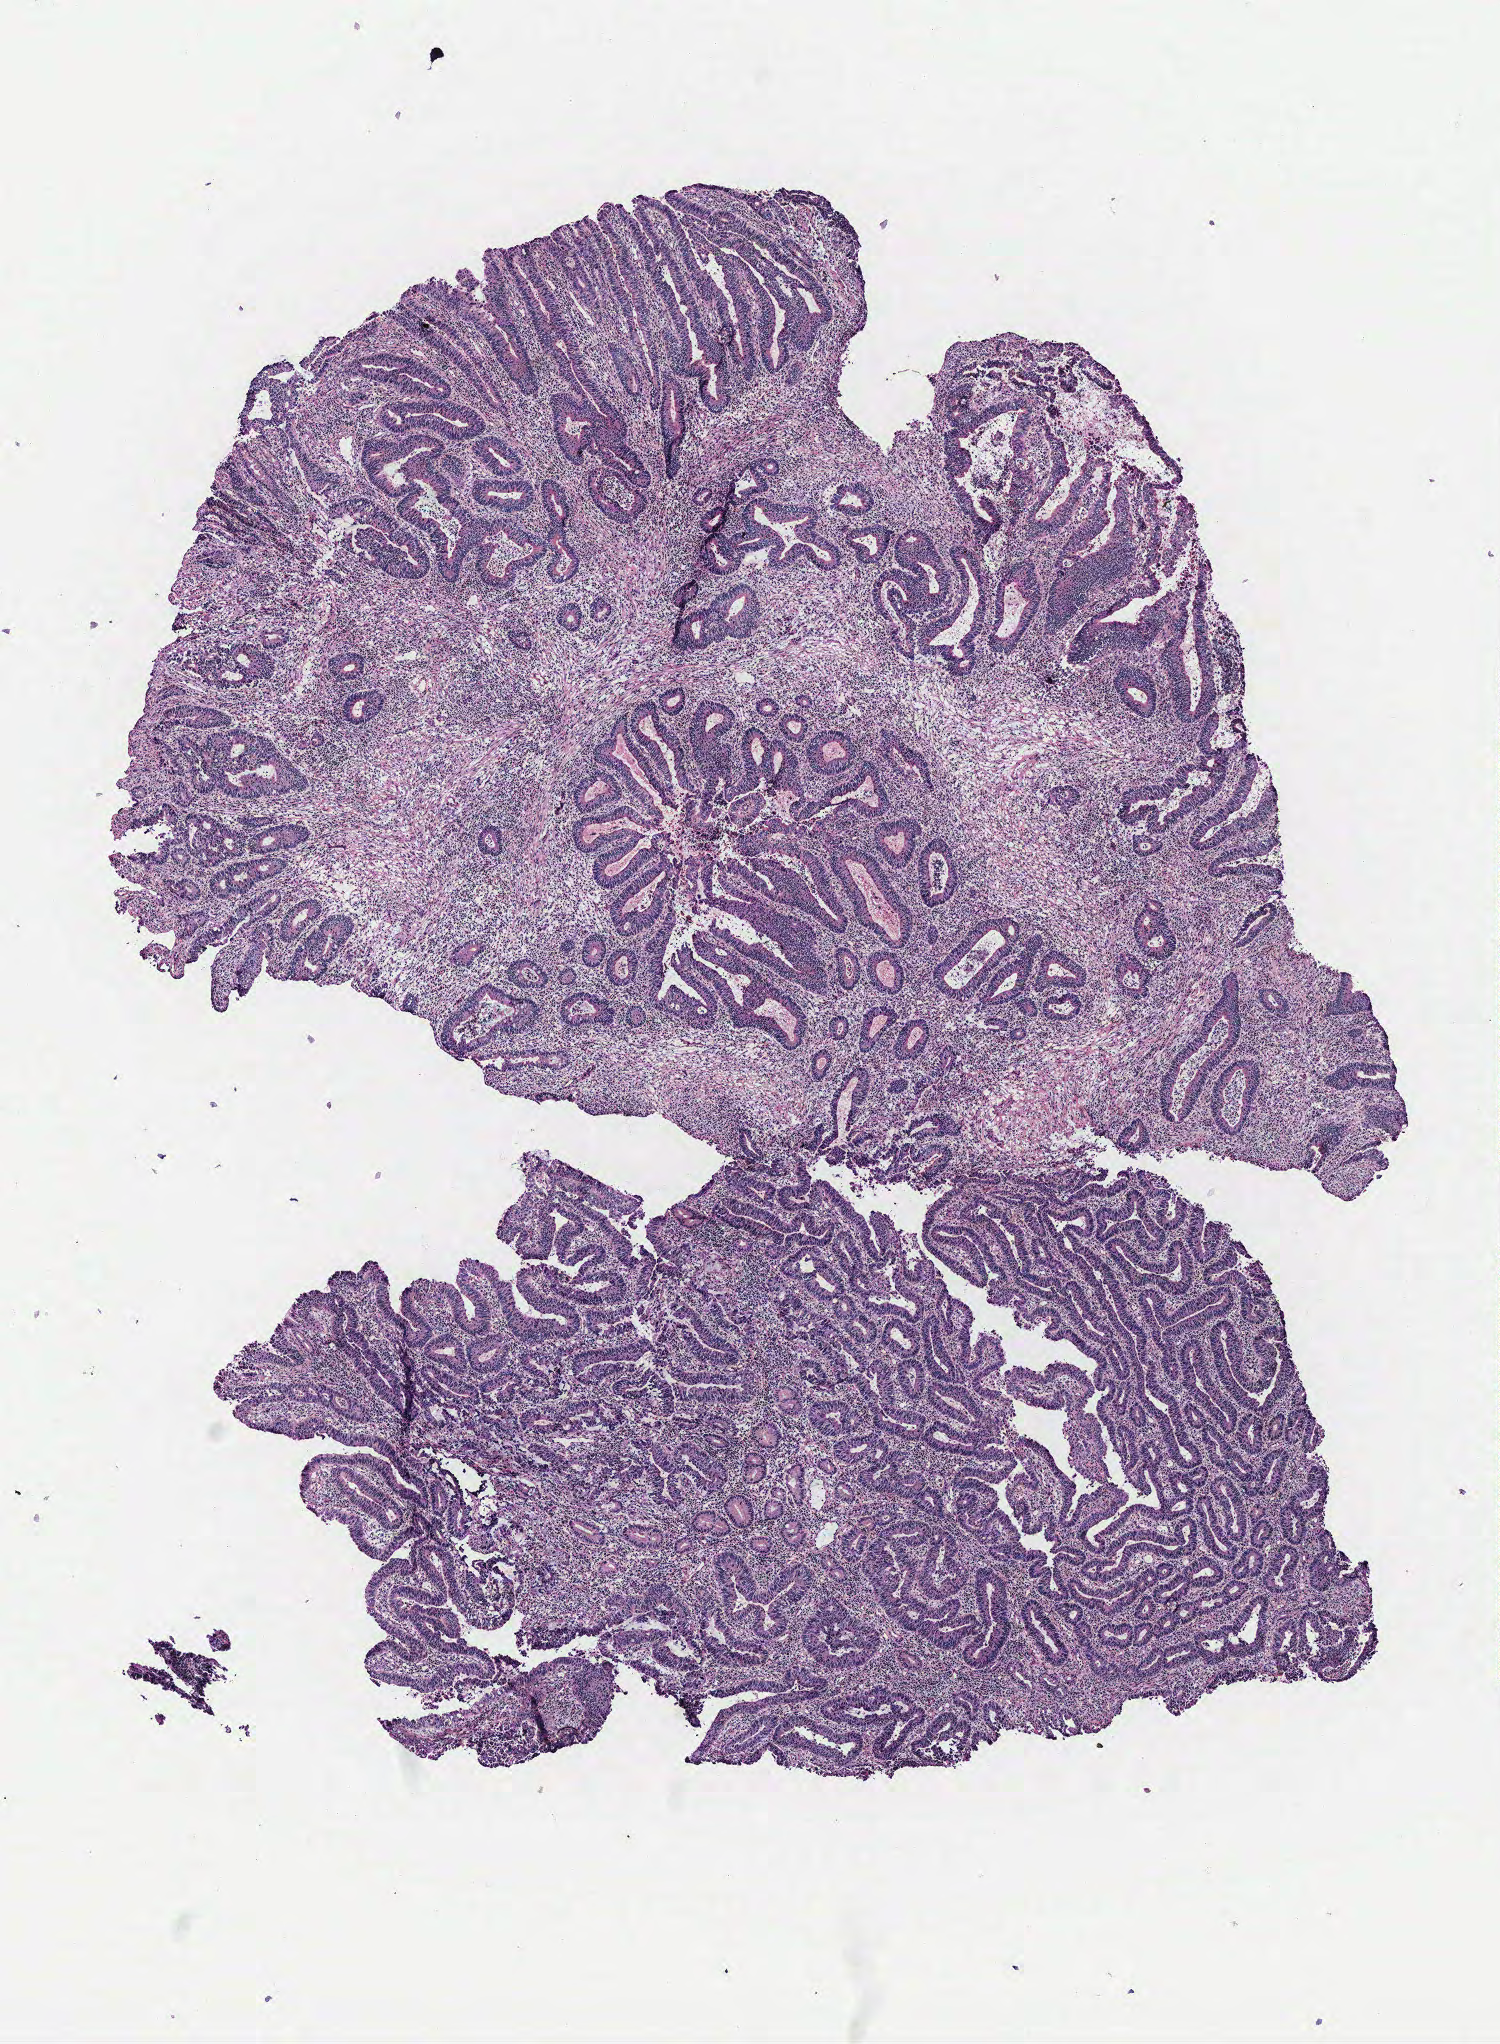
H&E whole-slide image — shown as a low-resolution overview of the whole scanned area (about 6.0 x 8.2 mm), colon, tissue type not recorded.
• patient diagnosis (cohort enrolment): colon cancer (colon)